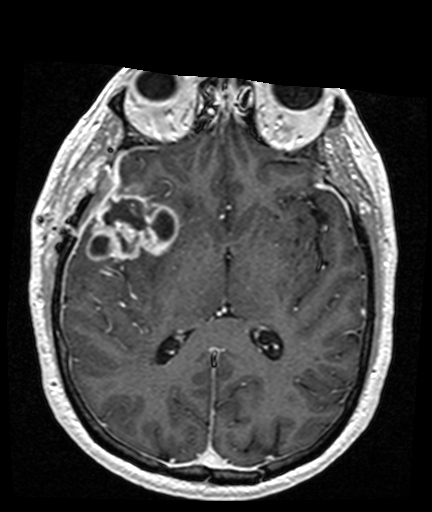
Brain MRI from a brain-tumour surgery series, one axial slice; slice 84 of 176 in the series (ordered by position); T1-weighted post-contrast; 1 mm slice thickness; 432 × 512 image matrix. From the clinical record (not read from this slice): histopathology: Glioblastoma; WHO grade: 4; IDH mutation: no; tumour location: Right Frontal Temporal, Posterior Sylvian Fissure.
Annotated regions visible in this slice (expert manual segmentation):
- tumour: box from (x=85, y=182) to (x=180, y=262) px